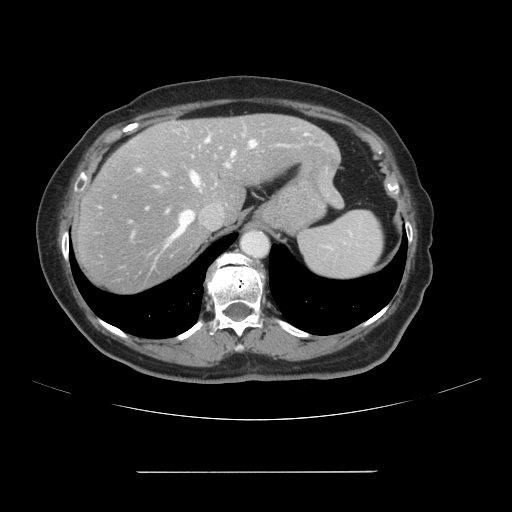
Contrast-enhanced abdominal CT, one axial slice; position 81 of 111 along the scan axis; intravenous contrast given; soft-tissue window (W 400 / L 40 HU); 2.5 mm slice thickness; 512 × 512 image matrix. Female patient, age 74 years. From the clinical record (not read from this slice): diagnosis: colorectal cancer liver metastases, imaged before liver resection.
Structures marked on this image (outlined manually by an expert reader):
- hepatic veins: bounding box [x1, y1, x2, y2] px = [156, 139, 256, 260]
- liver: [73, 115, 336, 294]
- planned liver remnant (the part of the liver to remain after resection): [160, 115, 337, 220]
- portal vein (with intrahepatic branches): [139, 137, 229, 226]